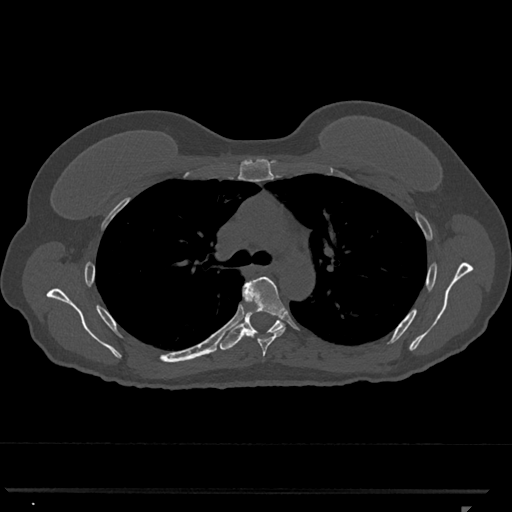
CT including the spine, one axial slice; position 787 of 793 along the scan axis; reconstruction kernel Br40s/3; 120 kVp; bone window (W 1800 / L 400 HU); 0.5 mm slice thickness; 512 × 512 image matrix. Patient: female, 62 years. From the clinical record (not read from this slice): primary cancer: renal.
Structures marked on this image (semi-automatically segmented with operator editing):
- T5 vertebra: bounding box <241,277,288,357> (left, top, right, bottom; pixels)
- T6 vertebra: <219,282,284,350>